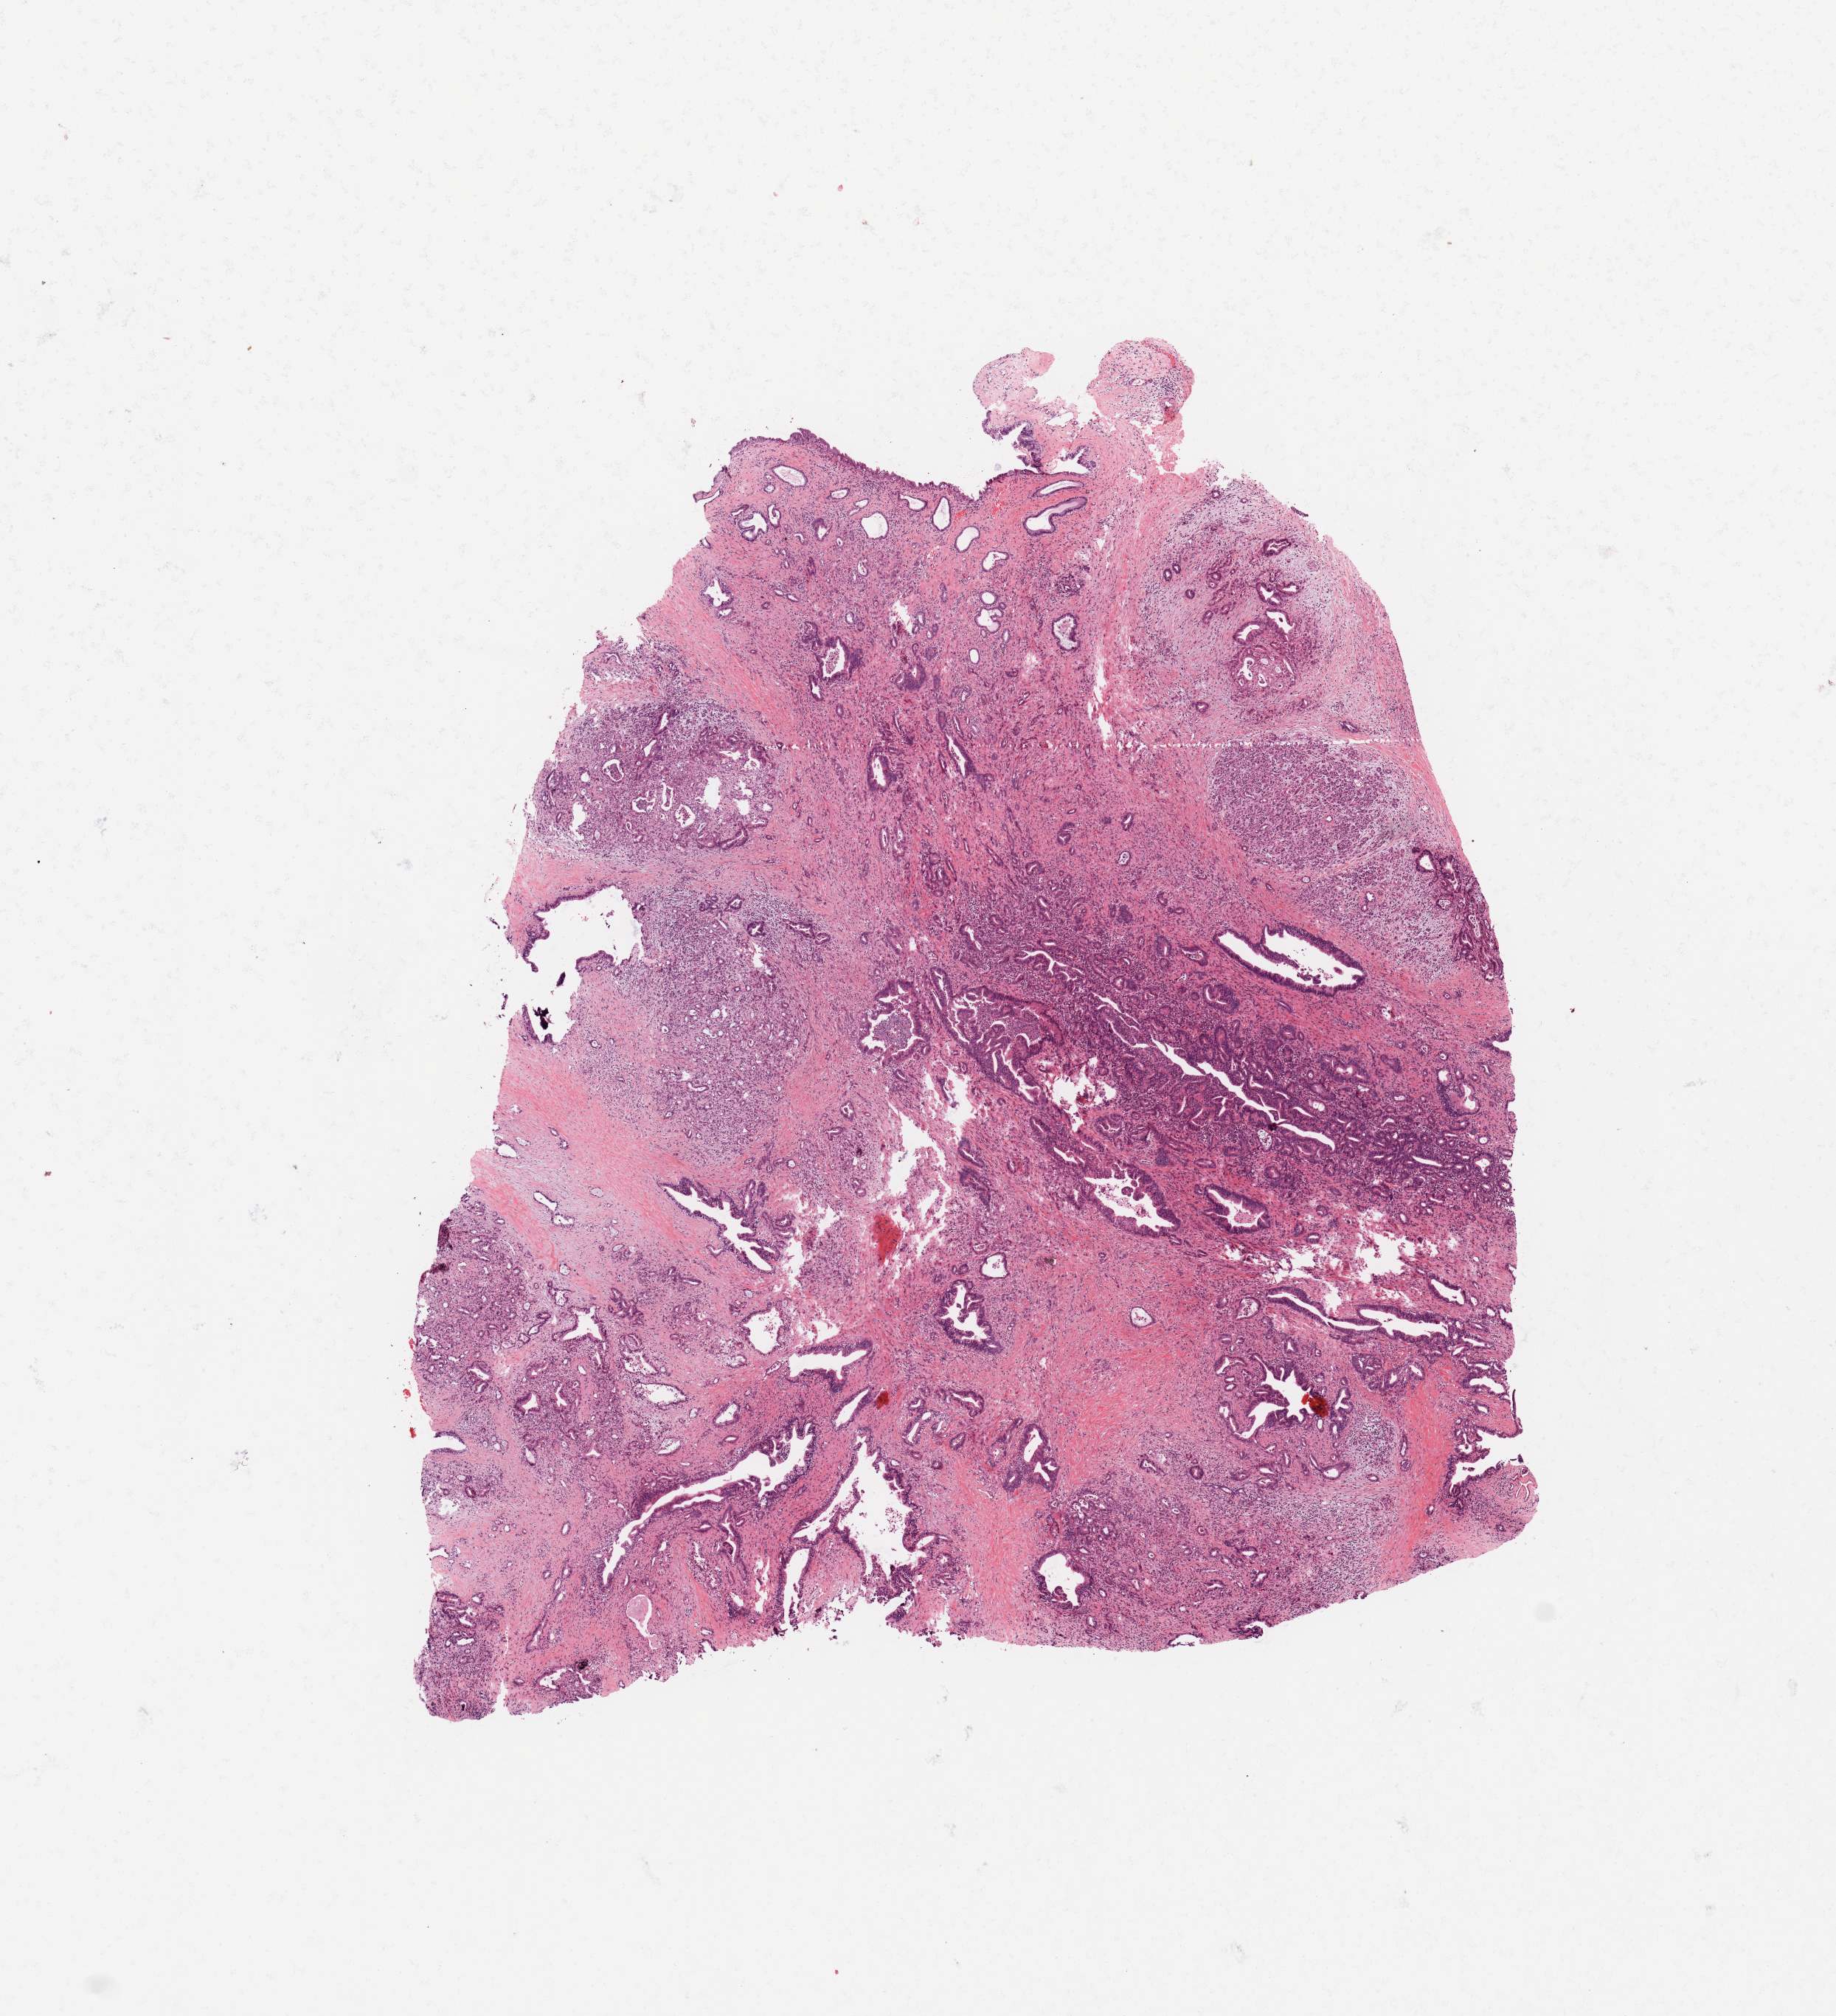
Whole-slide histology image, H&E, low-resolution overview of the scanned area, about 9.8 x 10.8 mm, tumour tissue sample, sampled site: pancreas. 69-year-old male patient. Histologic grade: G2 (moderately differentiated). Slide review estimates, as recorded: tumour nuclei 60%, necrosis 0%.
Histologic diagnosis: Infiltrating duct carcinoma, NOS. AJCC pathologic stage: IIB. Primary tumour site (as recorded): head.